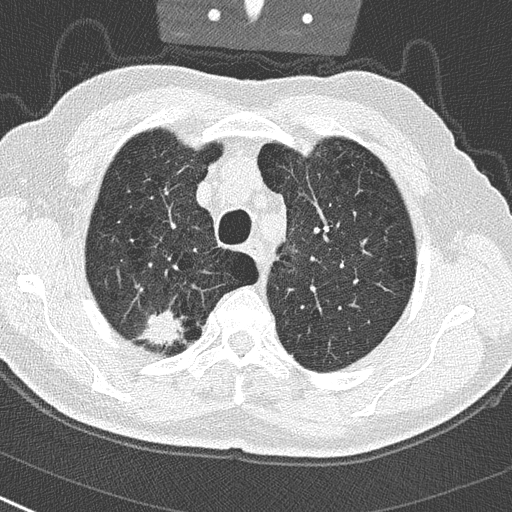
Low-dose screening chest CT, axial slice; first (baseline) screen; lung window (W 1500 / L -600 HU); lung (sharp) reconstruction kernel (B50f); 512 × 512 image matrix. Male participant, aged 65 years at enrolment.
Expert-annotated lung lesion, bounding box (x1, y1, x2, y2) in pixels: (134, 302, 188, 353). Screening reader's record for this exam (one nodule recorded; not confirmed to be the boxed lesion): non-calcified nodule or mass ≥4 mm, right upper lobe, 24 × 19 mm, spiculated (stellate) margins, soft tissue attenuation. Official screen result: positive, change unspecified: nodule(s) >= 4 mm or enlarging nodule(s), mass(es), or other non-specific abnormalities suspicious for lung cancer. Lung cancer was diagnosed 32 days after this screen: non-small cell carcinoma, right upper lobe, poorly differentiated (G3), stage IA (AJCC 6th edition), 29 mm at pathology.